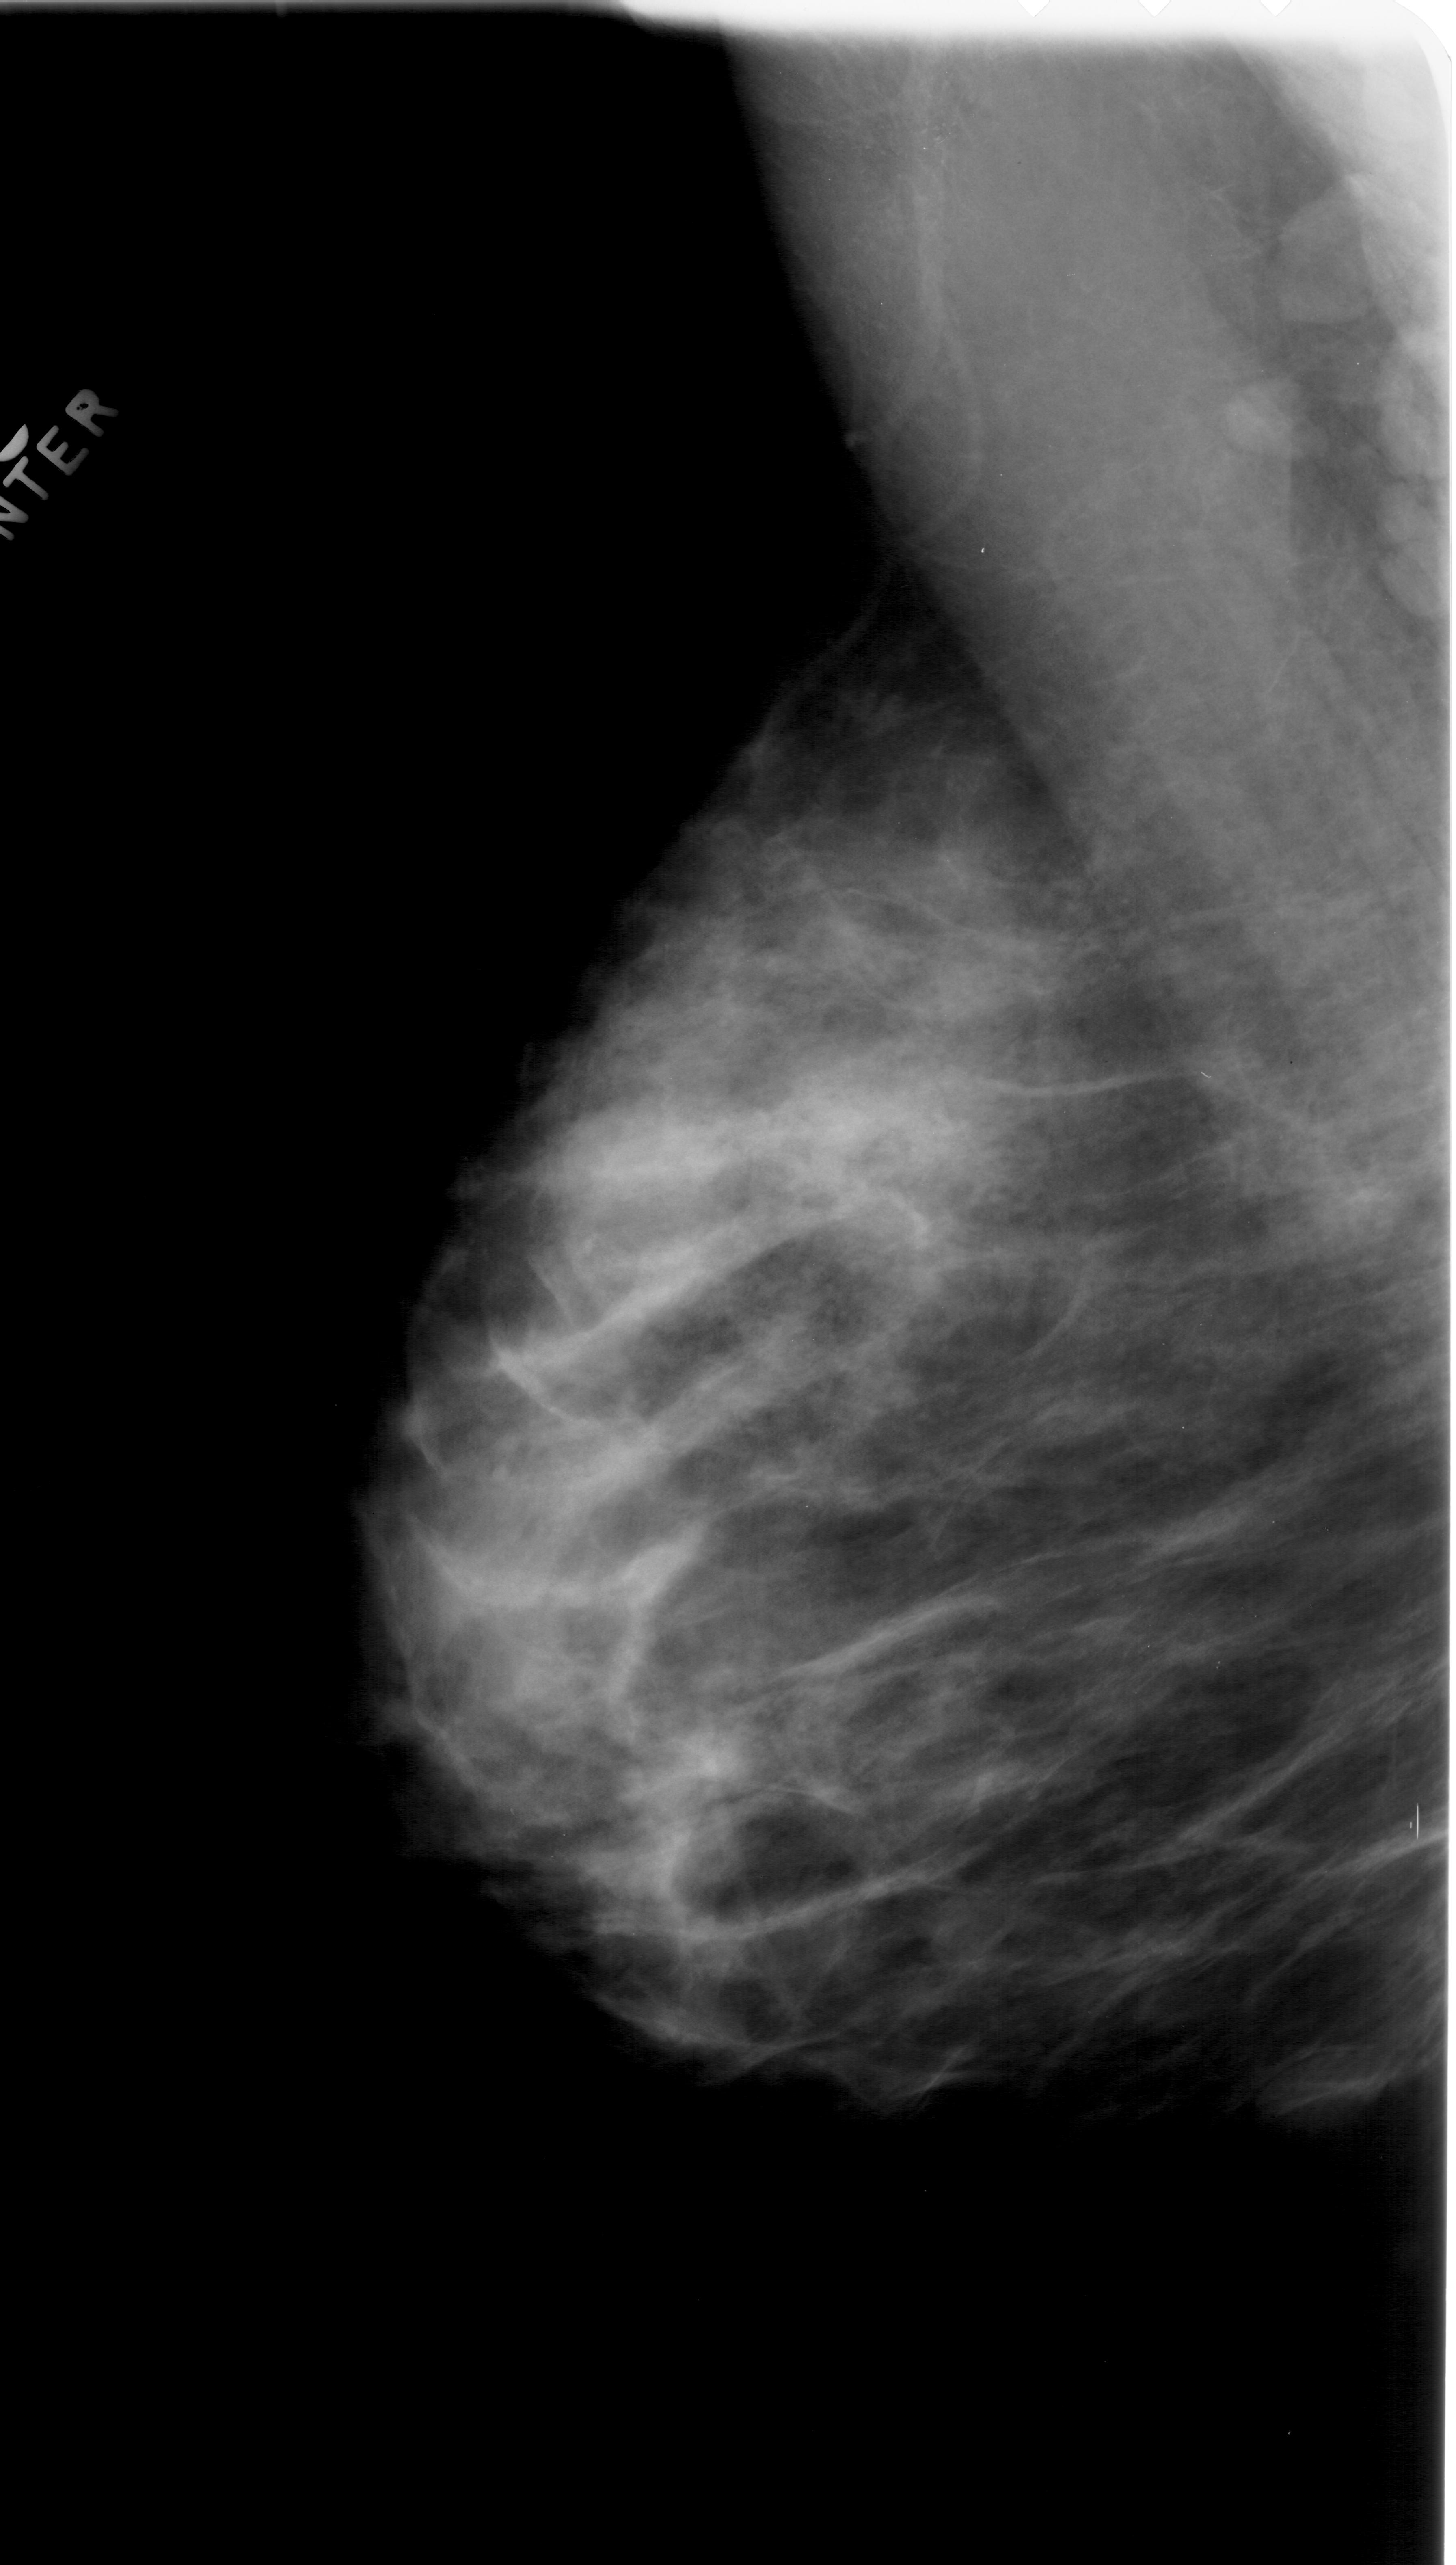
Digitized screen-film mammogram; left breast; mediolateral oblique (MLO) view; breast composition: extremely dense (BI-RADS density category 4 of 4).
Abnormality record for this image: mass, shape oval, margins circumscribed; BI-RADS assessment category 3; subtlety rating 3 on a 1 (subtle) to 5 (obvious) scale; pathology result (as recorded, not read from the image): benign.